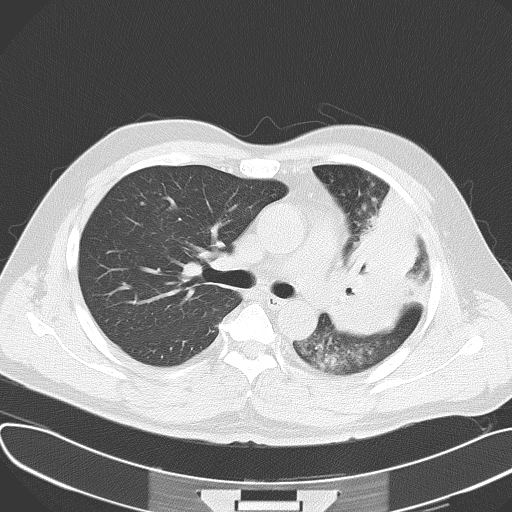
Chest CT, one axial slice; slice 40 of 62 in the series (ordered by position); reconstruction kernel B70f; 120 kVp; lung window (W 1500 / L -600 HU); 5 mm slice thickness; 512 × 512 image matrix. Patient: male, 48 years. From the clinical record (not read from this slice): clinical TNM (as recorded): T4 N0 M0.
Structures marked on this image (bounding box drawn by a radiologist):
- lung tumour (recorded histology: adenocarcinoma): bounding box <328,177,418,342> (left, top, right, bottom; pixels)